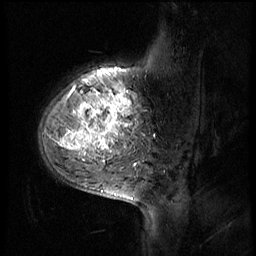
Breast MRI (dynamic contrast-enhanced), one sagittal slice. Position 13 of 56 along the scan axis. 4 images stored at this slice position (order not interpretable as contrast timing). 1.5 T. TE 4.2 ms, TR 8.9 ms. 2.5 mm slice thickness. 256 × 256 image matrix, field of view 220 × 220 mm. Patient: female, 51 years. From the clinical record (not read from this slice): setting: breast cancer imaged before/during neoadjuvant chemotherapy; receptor status: triple-negative.
Outlined on this slice (semi-automatic segmentation, software-assisted and operator-edited):
- analysis volume of interest (the breast-tissue region the enhancement analysis was run in; not a lesion): bounding box (x1, y1, x2, y2) in pixels: (39, 70, 150, 173)
- tumour enhancement mask (voxels above the 140 % enhancement threshold inside the analysis volume of interest): (61, 86, 132, 155)